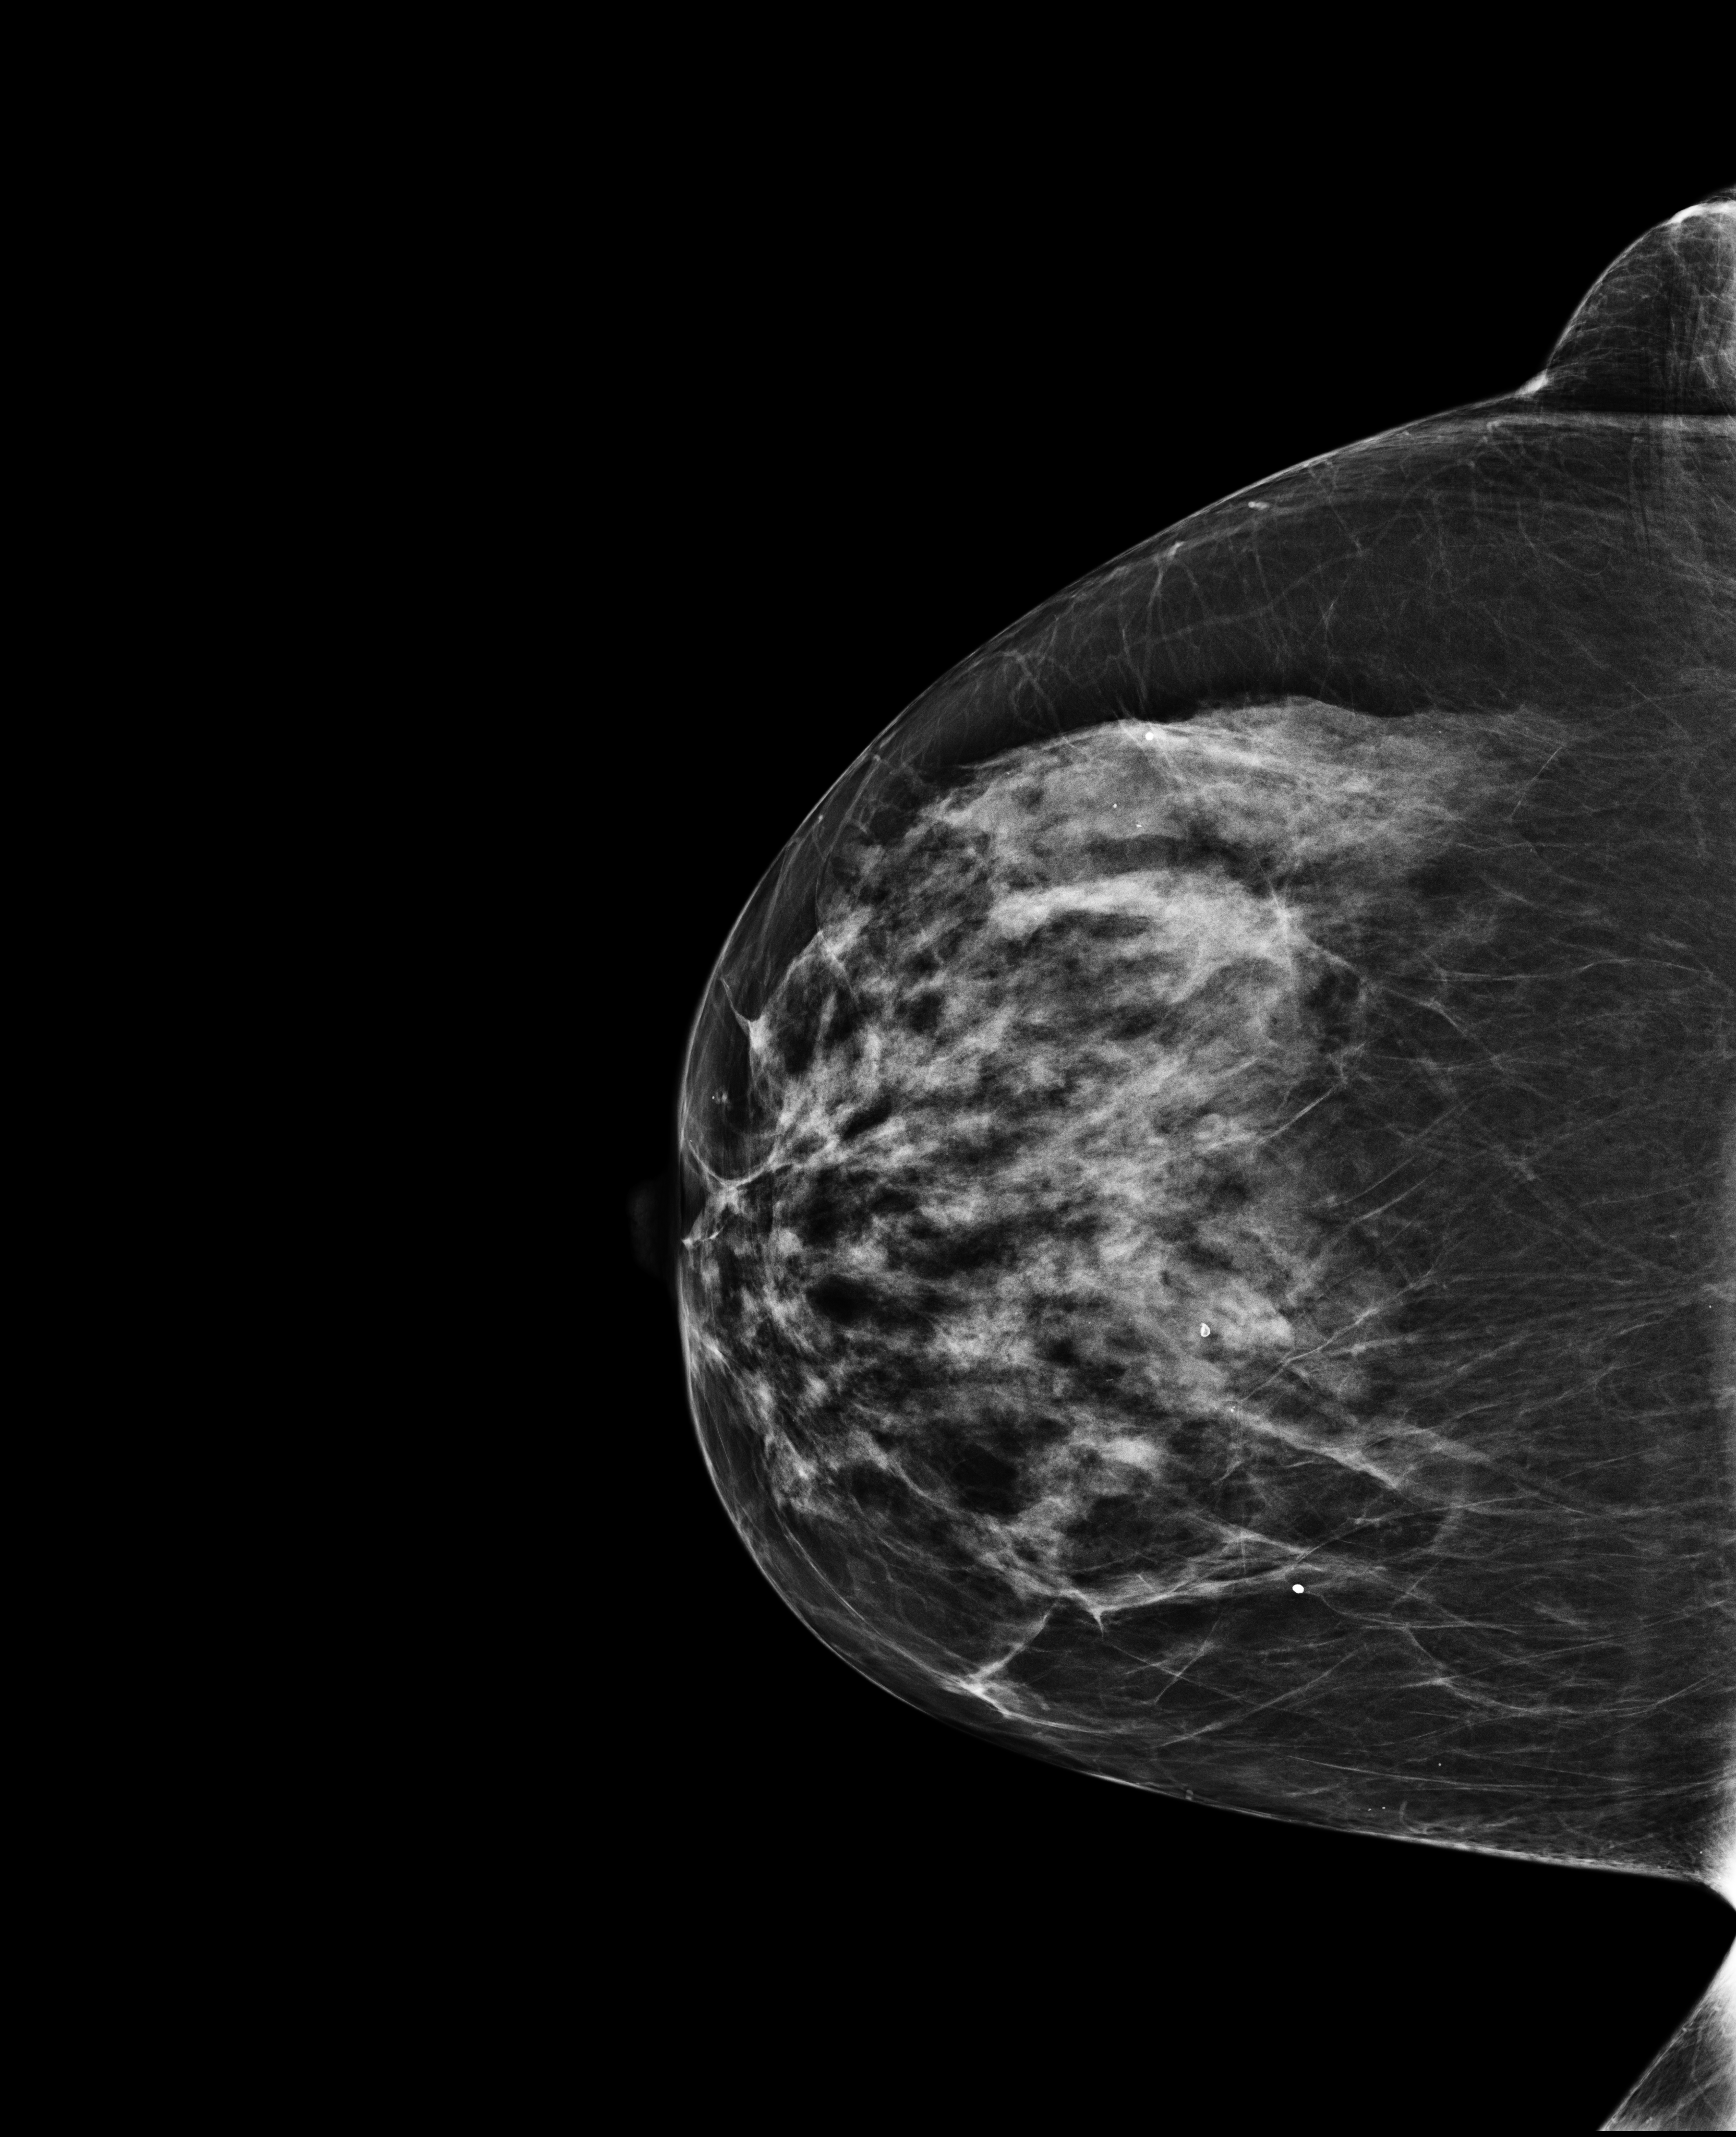
Screening examination; compressed breast thickness 60 mm. Patient aged 63 years (female).
Image type: full-field digital mammogram. Breast: right. Projection: craniocaudal (CC) view.